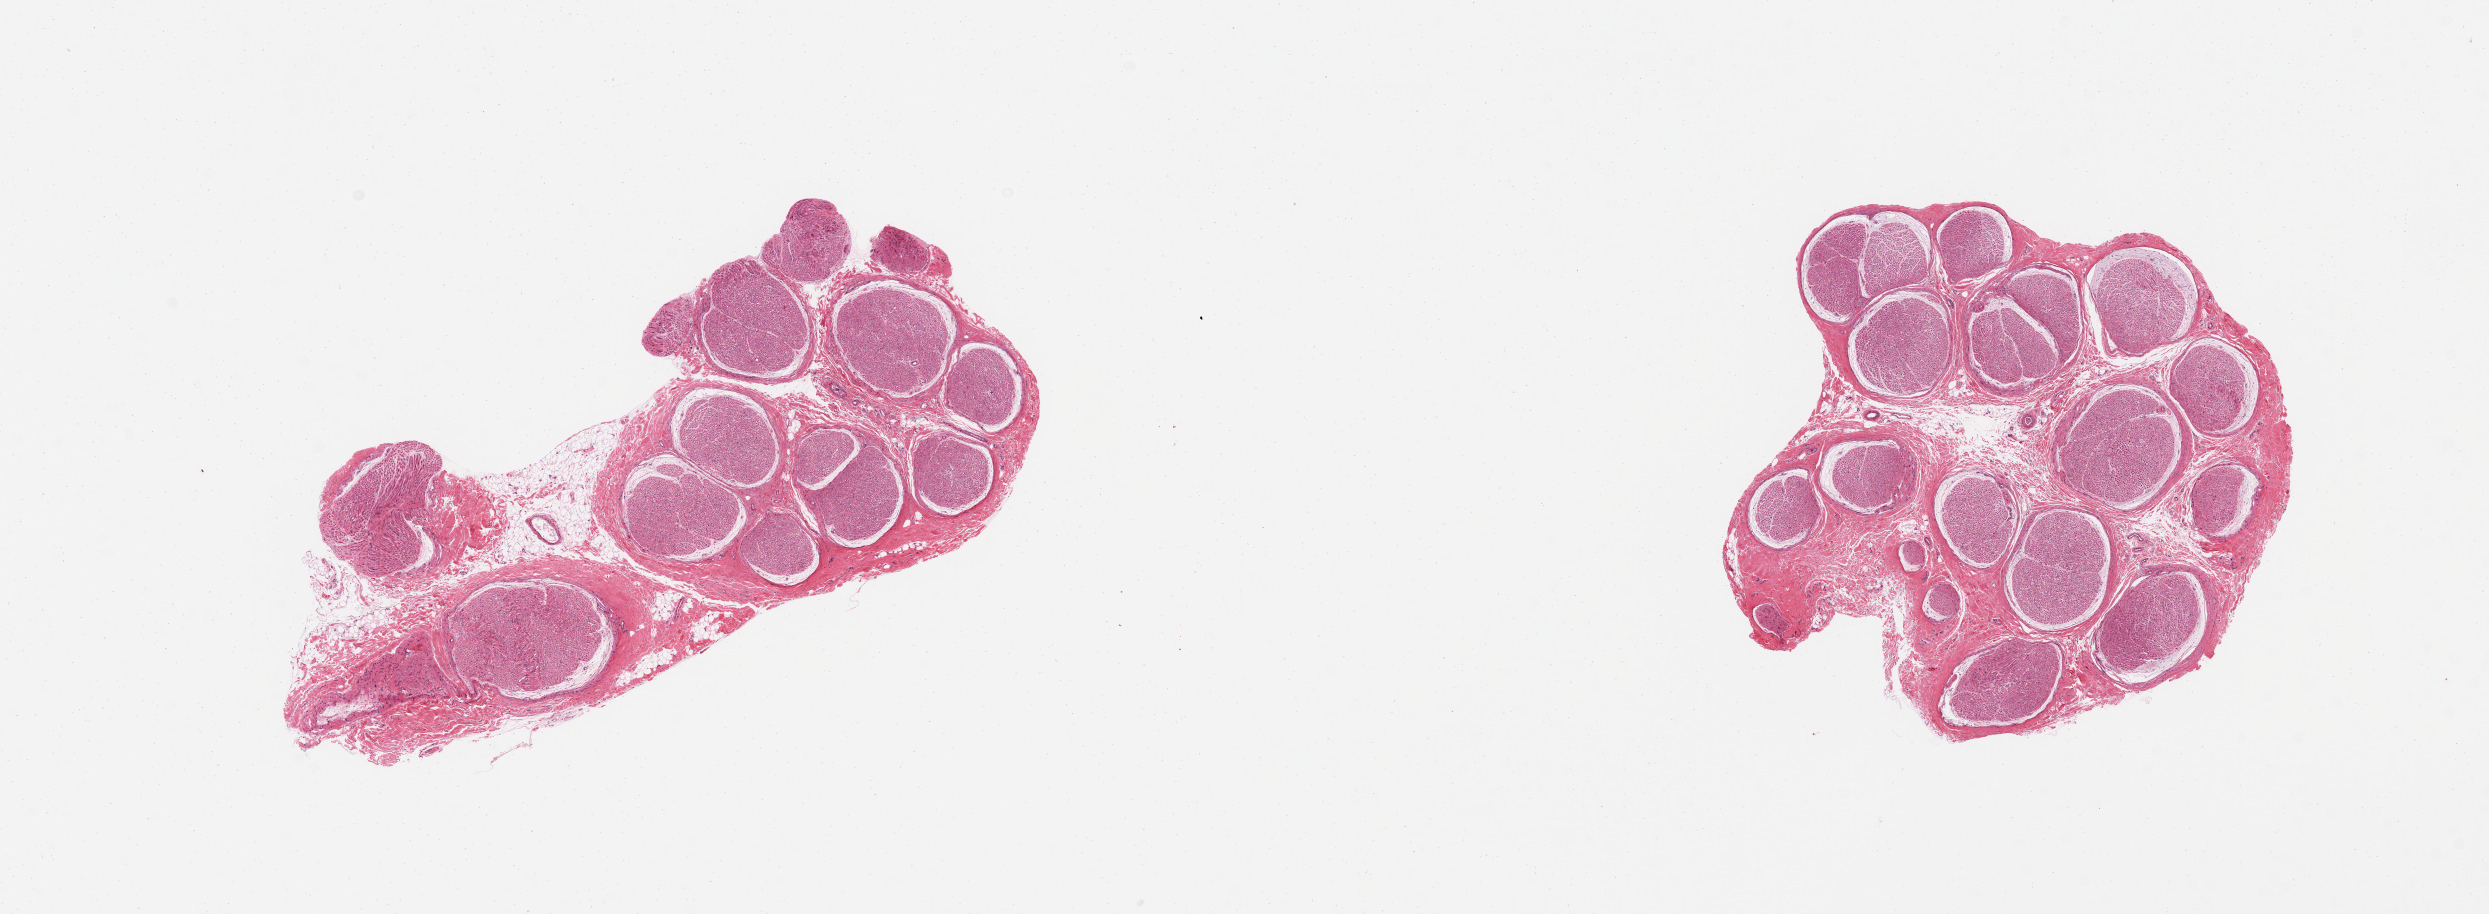
Digitized haematoxylin and eosin-stained section, brightfield — low-resolution overview of the scanned area, about 19.7 x 7.2 mm (from a 20x scan); PAXgene-fixed paraffin-embedded (PFPE) section; section of tibial nerve (target tissue); donor tissue sample.
Review note (as recorded): 2 pieces; well trimmed.